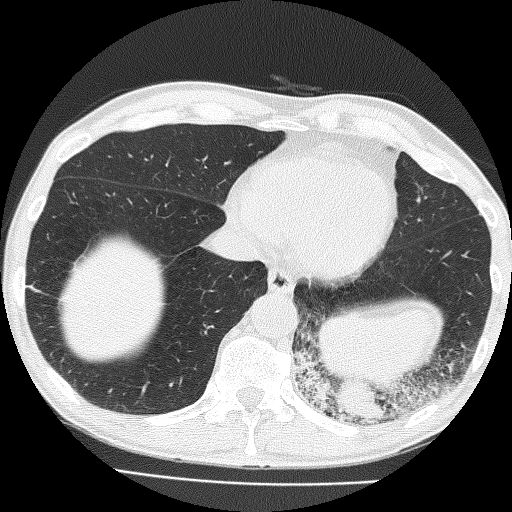
Chest CT (low-dose screening protocol), one axial image; first (baseline) screen; lung window (W 1500 / L -600 HU); 2 mm slice thickness; slice 113 of 160 in the series. Male, age 58 years at enrolment. Current smoker at enrolment.
Lesion marked by an expert reader, bounding box (x1, y1, x2, y2) in pixels: (288, 291, 432, 436). The screening reader recorded 2 non-calcified nodules or masses ≥4 mm on this exam (left lower lobe, left upper lobe); which of them this box marks is not recorded. Official screen result: positive, change unspecified: nodule(s) >= 4 mm or enlarging nodule(s), mass(es), or other non-specific abnormalities suspicious for lung cancer. Participant outcome: lung cancer diagnosed 39 days after this screen — non-small cell carcinoma, left lower lobe, poorly differentiated (G3), stage IV (AJCC 6th edition), 74 mm at pathology.